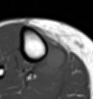
MRI of an extremity soft-tissue mass, one axial slice. Slice 26 of 54 in the series (ordered by position). MR volume resampled by the dataset authors to the PET/CT grid (not the native acquisition matrix). 3.27 mm slice thickness. 93 × 99 image matrix. Female patient. Case-level facts recorded for this patient, not image findings: histological type: undifferentiated – high grade; grade: high; site of the primary tumour: right thigh.
Structures marked on this image (expert contour drawn on MRI and transferred to this co-registered scan by the dataset authors):
- gross tumour volume (mass): bounding box (x1, y1, x2, y2) in pixels: (36, 29, 64, 72)